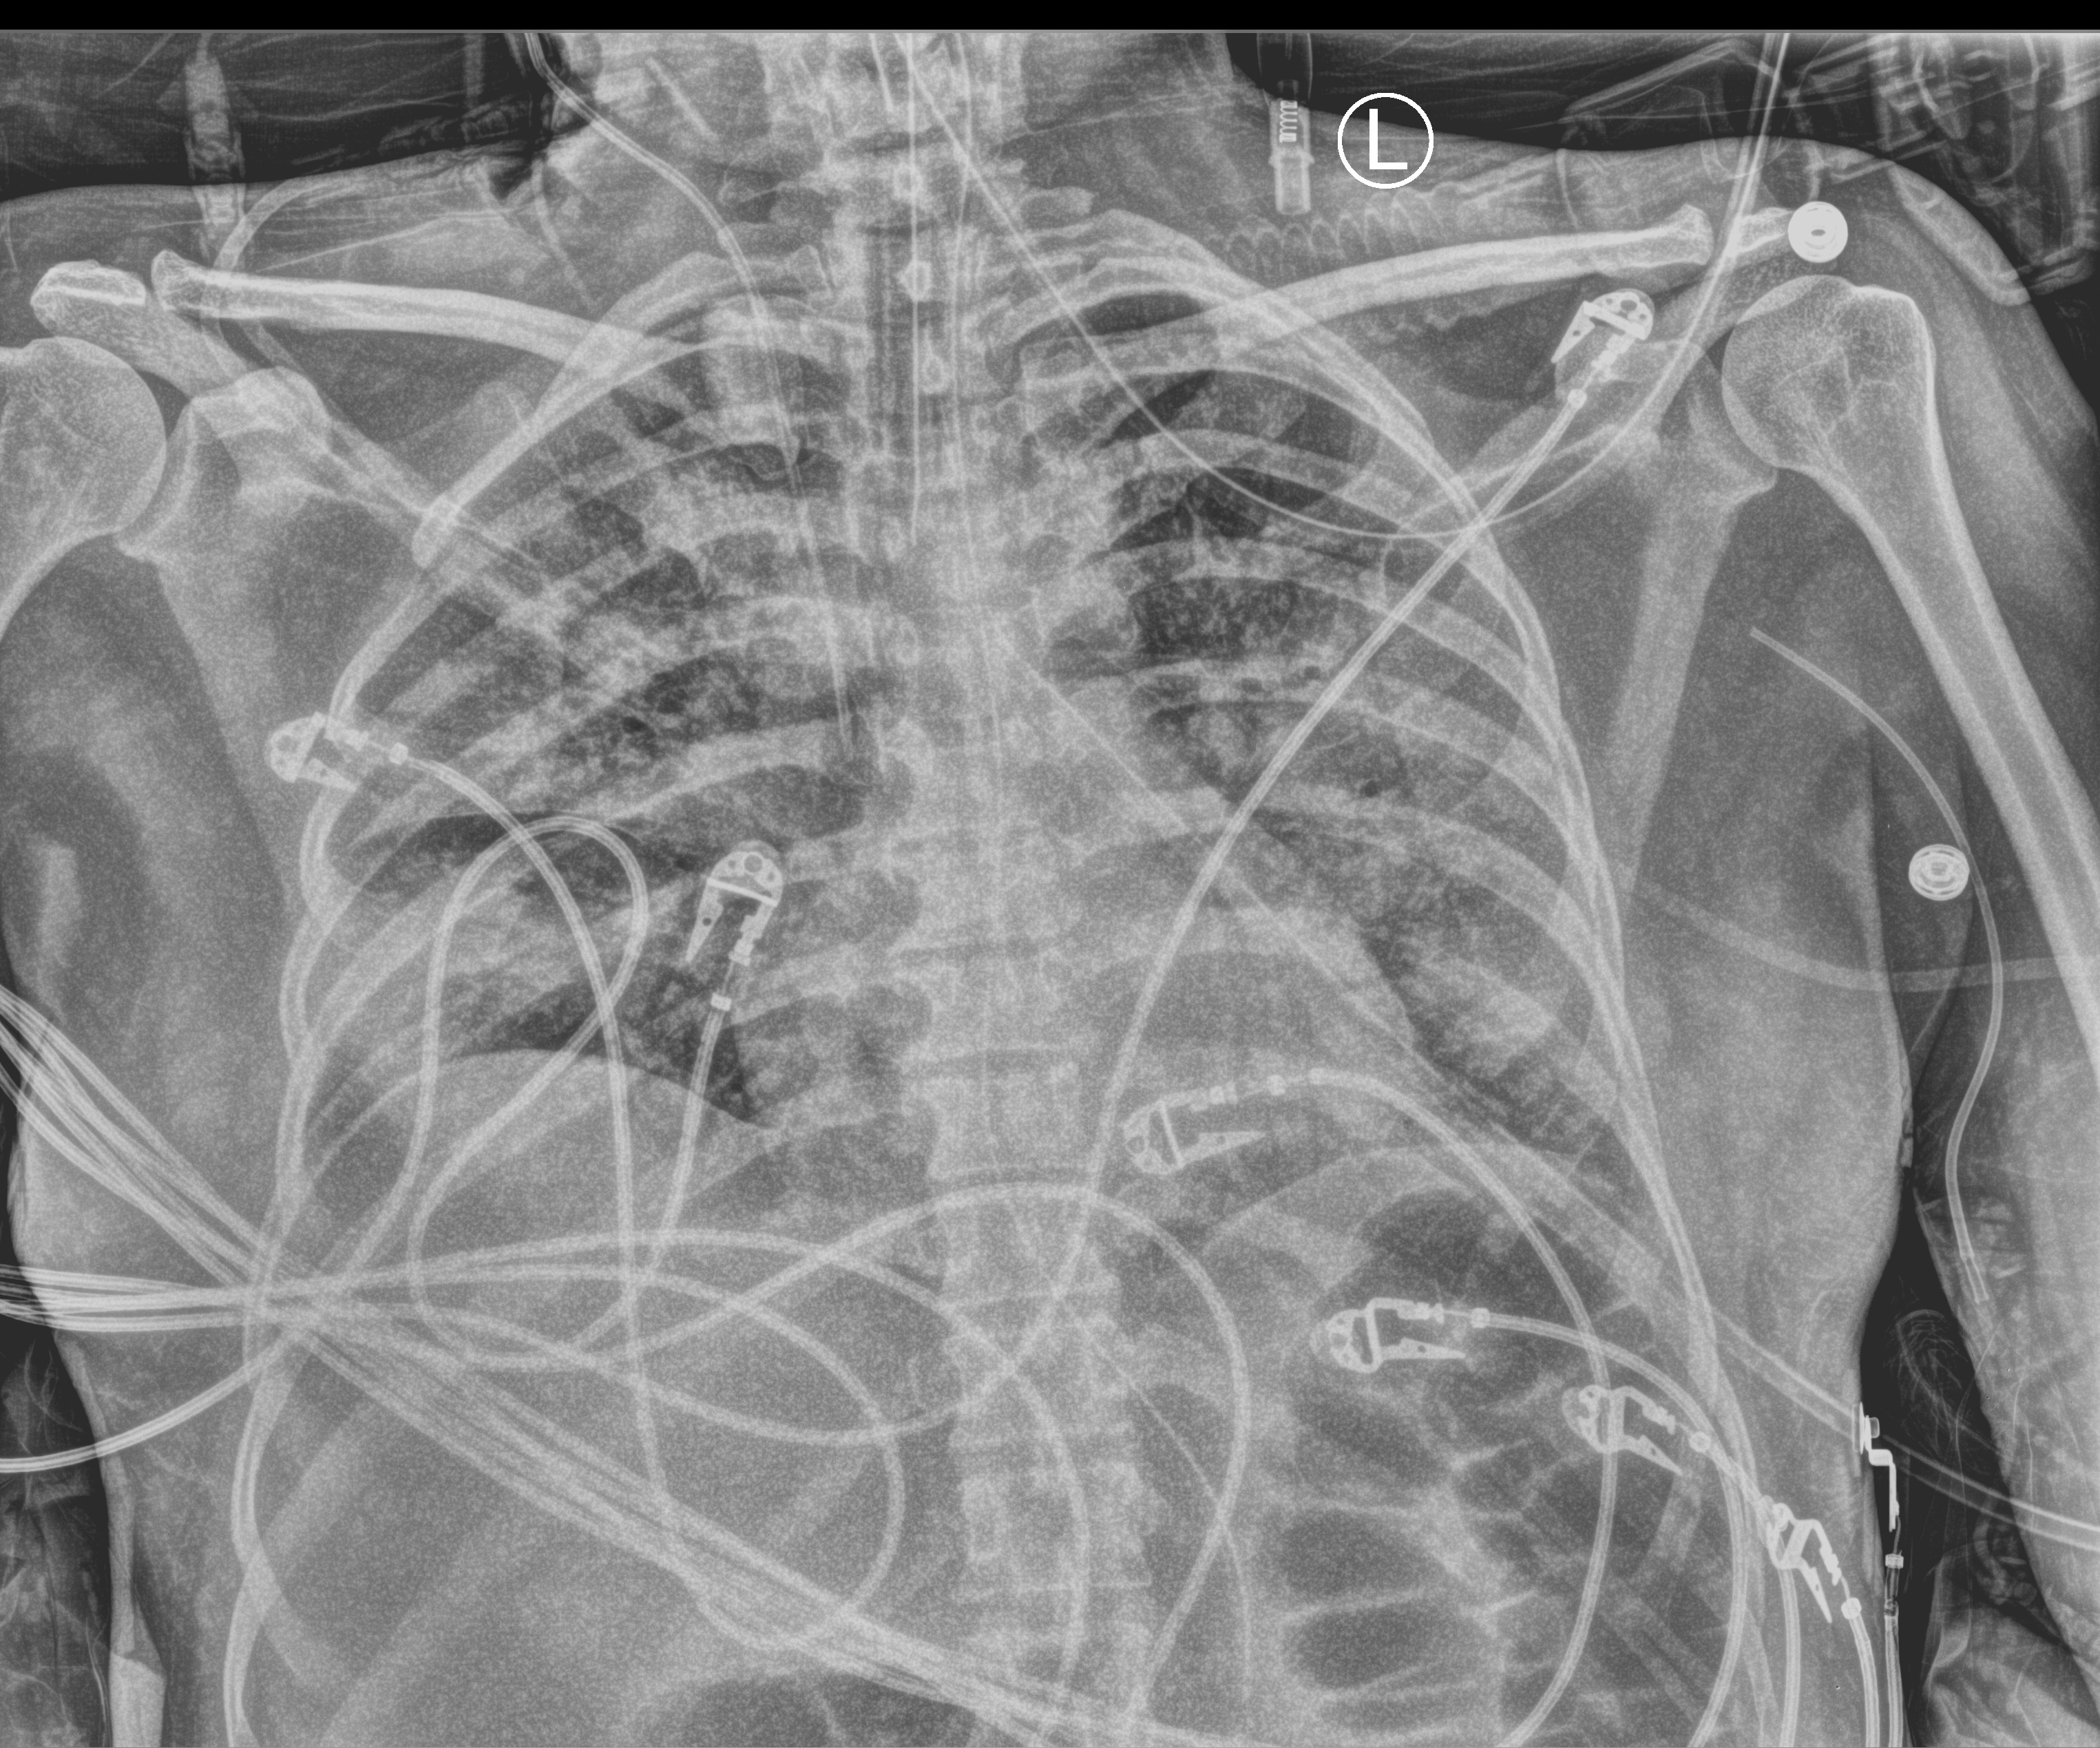
Portable chest radiograph, anteroposterior (AP) projection. Patient hospitalised with COVID-19; female, aged 18–59 years.
From the hospital-stay record, not from the radiograph (when in the stay this image was taken is not recorded):
- mechanically ventilated during this hospital stay: yes
- chronic kidney disease (admission record): no